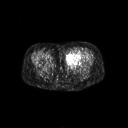
FDG PET of an extremity soft-tissue mass (from a PET/CT study), one axial slice. Slice 23 of 267 in the series (ordered by position). 128 × 128 image matrix, field of view 700 × 700 mm. Patient: female, 47 years. Case-level facts recorded for this patient, not image findings: histological type: myxofibrosarcoma; grade: intermediate; site of the primary tumour: left thigh.
Structures marked on this image (expert contour drawn on MRI and transferred to this co-registered scan by the dataset authors):
- gross tumour volume including surrounding oedema: bounding box <66,51,82,65> (left, top, right, bottom; pixels)
- gross tumour volume (mass): <66,51,82,64>